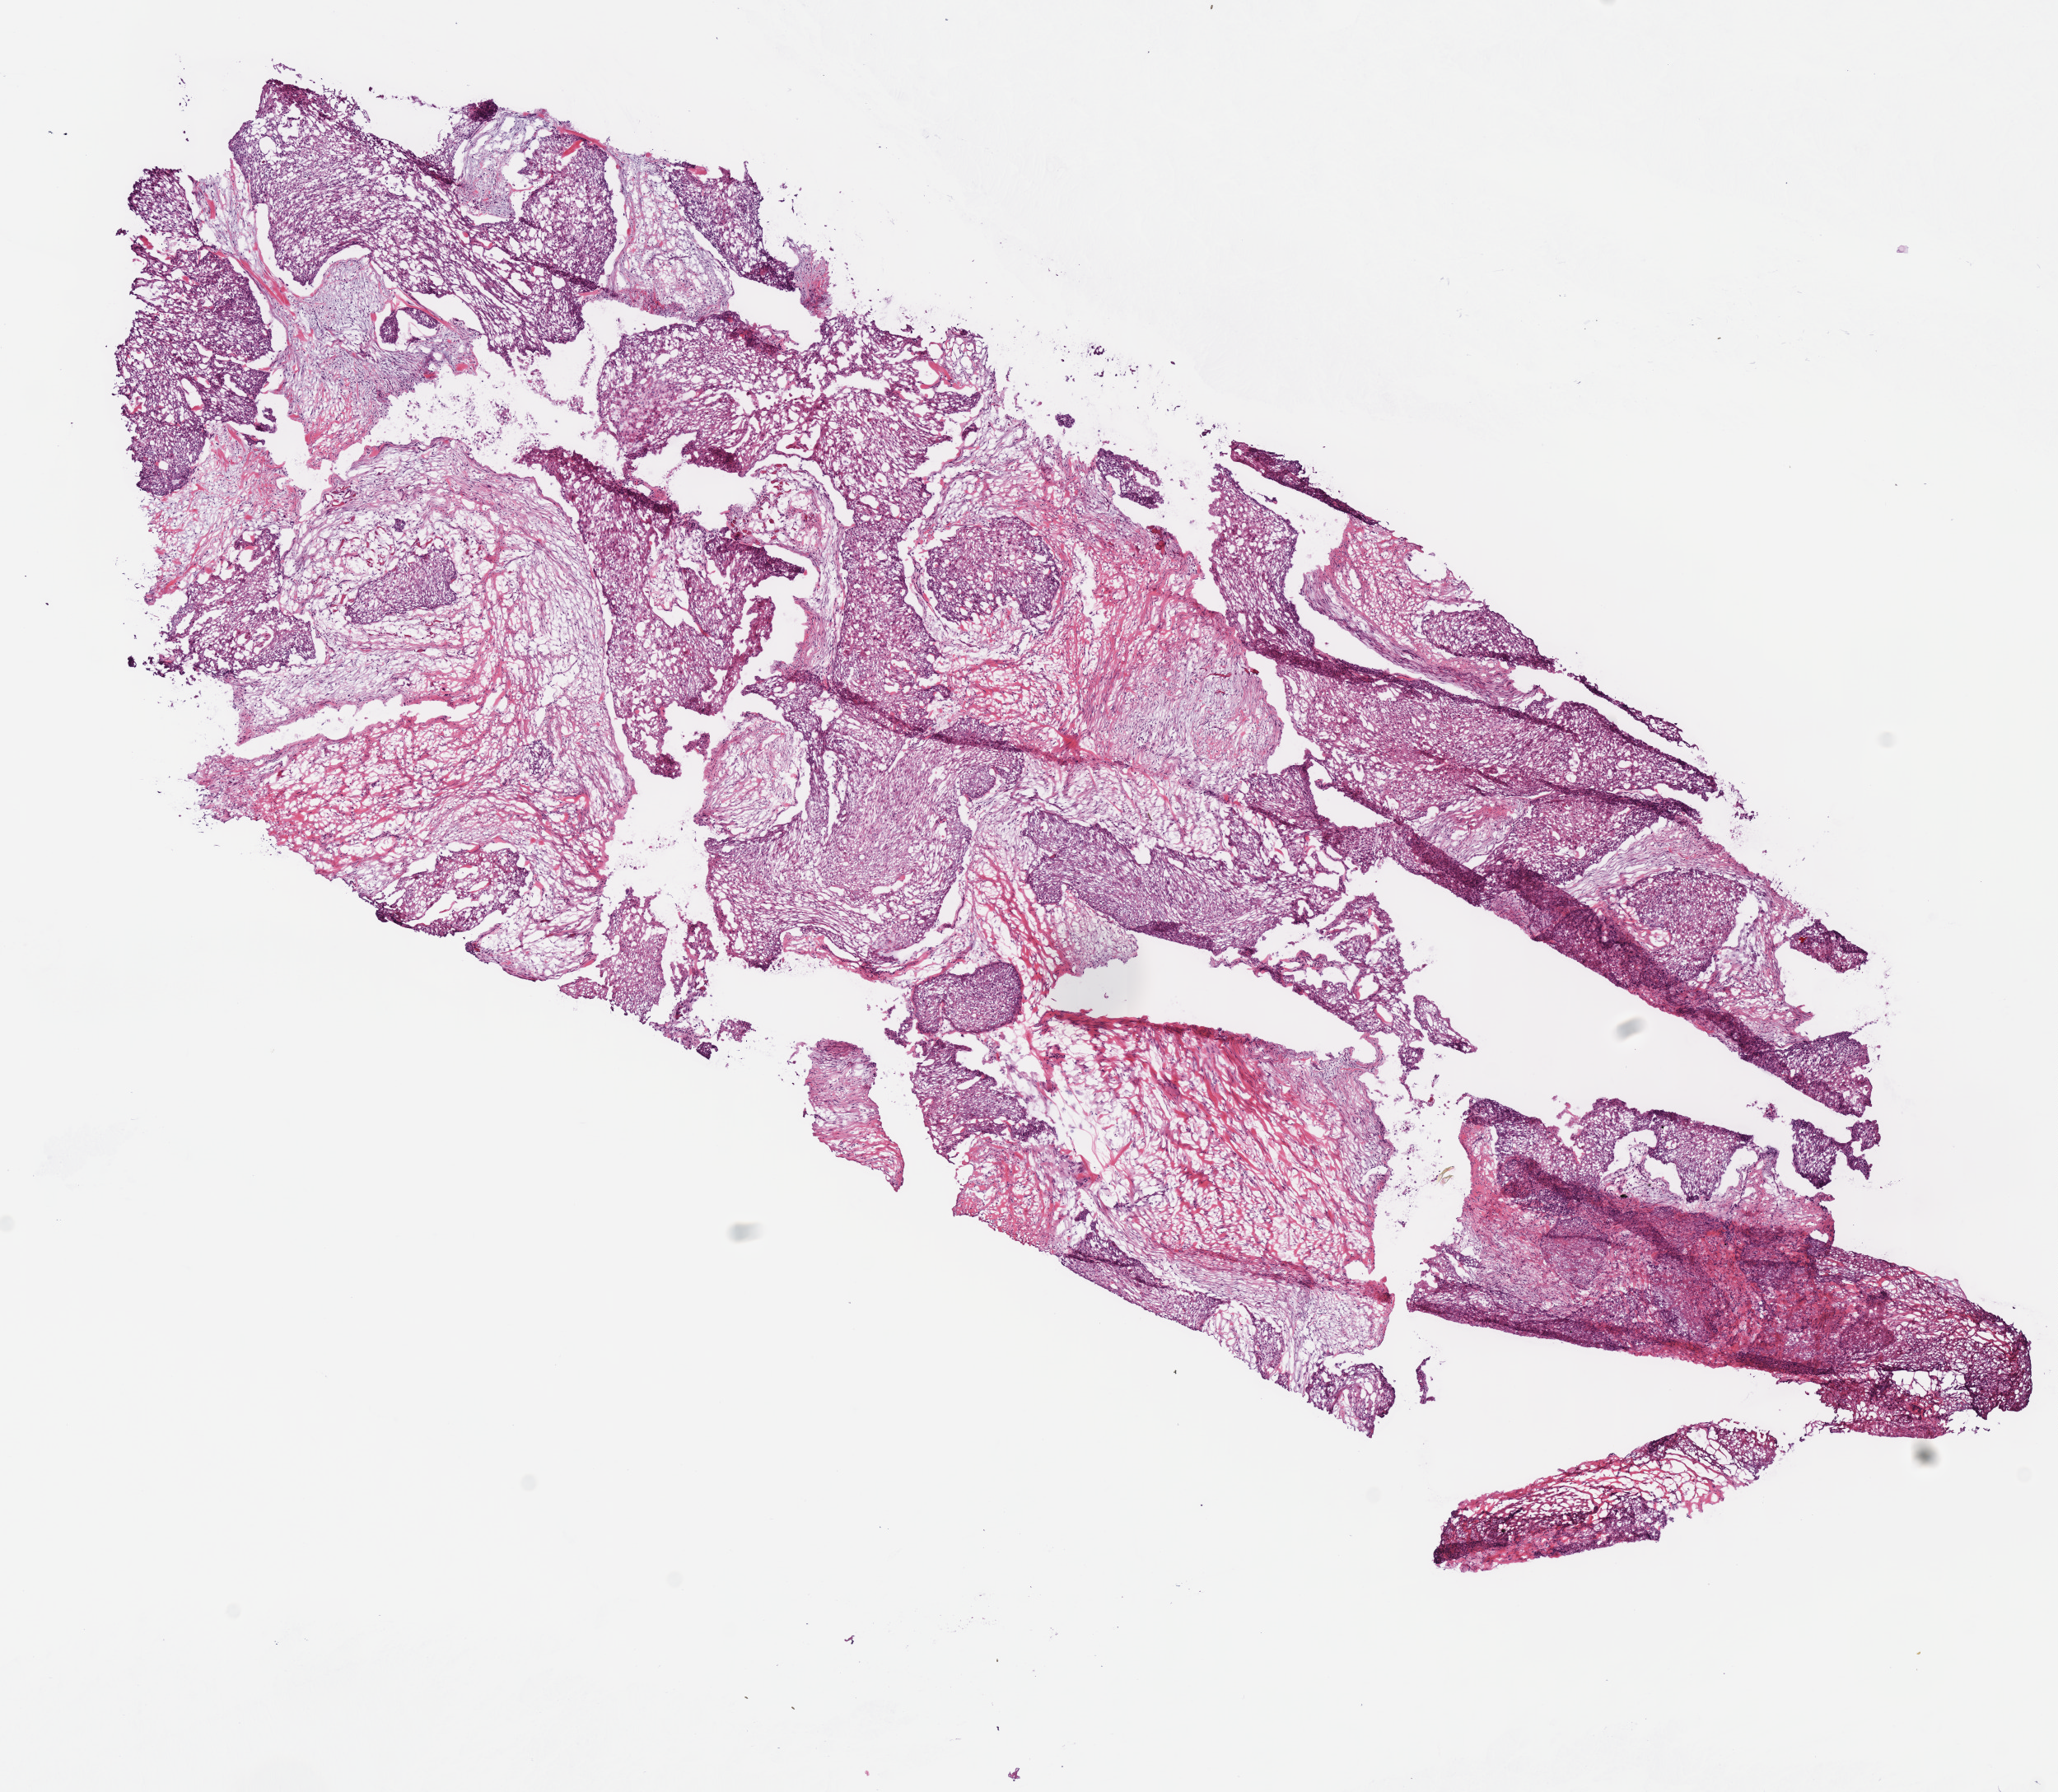
Hematoxylin and eosin (H&E) stained whole-slide image — whole scanned area (about 9.8 x 8.6 mm, acquisition: 40x scan) shown as a low-resolution overview; frozen section; primary tumour sample from the head and neck. Male patient; age at initial diagnosis 78 years. Histologic grade: G2 (moderately differentiated). Pathologist review of this section (percent, as recorded): tumour cells 55%, tumour nuclei 75%, normal cells 0%, stromal cells 45%, necrosis 0%. Infiltration values recorded for this section: lymphocyte infiltration 2%, monocyte infiltration 0%, neutrophil infiltration 0%.
* diagnosis: Squamous cell carcinoma, NOS (overlapping lesion of lip, oral cavity and pharynx)
* AJCC pathologic stage: IVA
* laterality: left
* TNM: T4a N2b